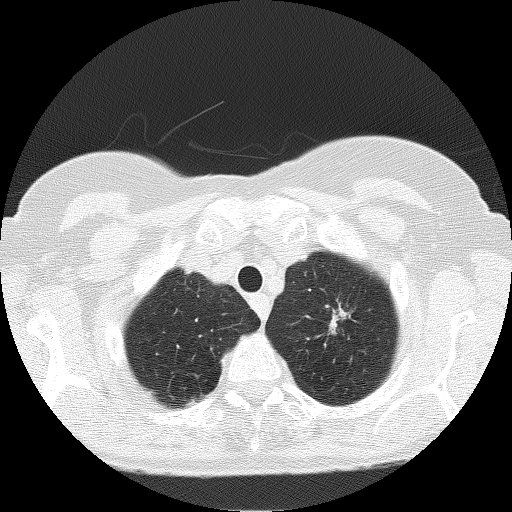
Low-dose screening chest CT, one axial slice. Slice 149 of 166 in the series (ordered by position). 120 kVp. Lung window (W 1500 / L -600 HU). 2 mm slice thickness. 512 × 512 image matrix, field of view 303 × 303 mm.
Annotated regions visible in this slice (manually delineated by an expert):
- lesion 3 (nodule, upper lobe of left lung): bounding box <329,308,348,332> (left, top, right, bottom; pixels)